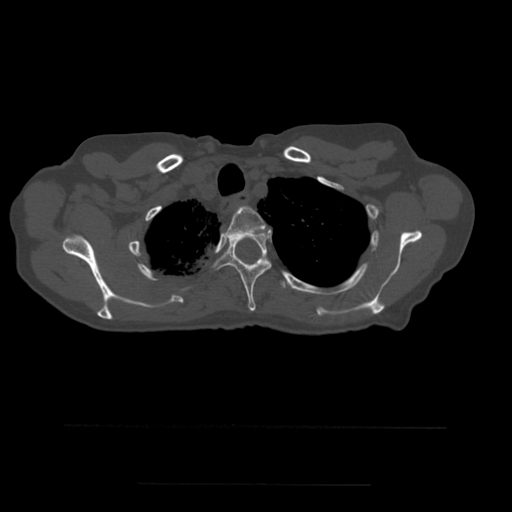
CT including the spine, one axial slice; position 423 of 544 along the scan axis; bone window (W 1800 / L 400 HU); 1.25 mm slice thickness; 512 × 512 image matrix, field of view 350 × 350 mm. Patient age 58 years. From the clinical record (not read from this slice): primary cancer: lung.
Outlined on this slice (semi-automatic segmentation, software-assisted and operator-edited):
- T2 vertebra: bounding box [x1, y1, x2, y2] px = [224, 206, 266, 240]
- T3 vertebra: [210, 232, 272, 311]
- T4 vertebra: [281, 277, 286, 289]